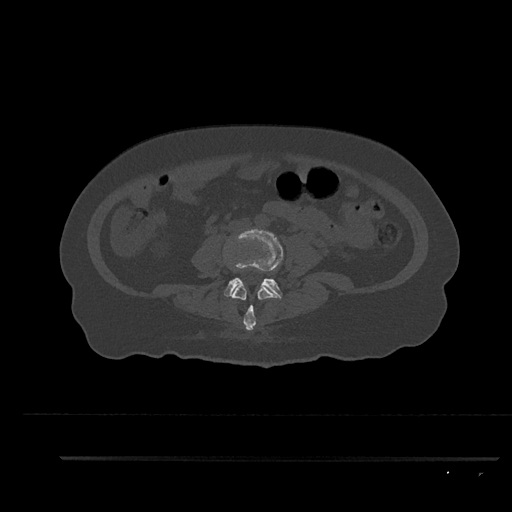
CT including the spine, one axial slice. Position 49 of 797 along the scan axis. 120 kVp. Bone window (W 1800 / L 400 HU). 0.5 mm slice thickness. 512 × 512 image matrix, field of view 408 × 408 mm. Patient: female, 44 years. Case-level facts recorded for this patient, not image findings: primary cancer: renal.
Annotated regions visible in this slice (semi-automatically segmented with operator editing):
- L3 vertebra: bounding box [x1, y1, x2, y2] px = [232, 285, 281, 331]
- L4 vertebra: [224, 228, 283, 299]